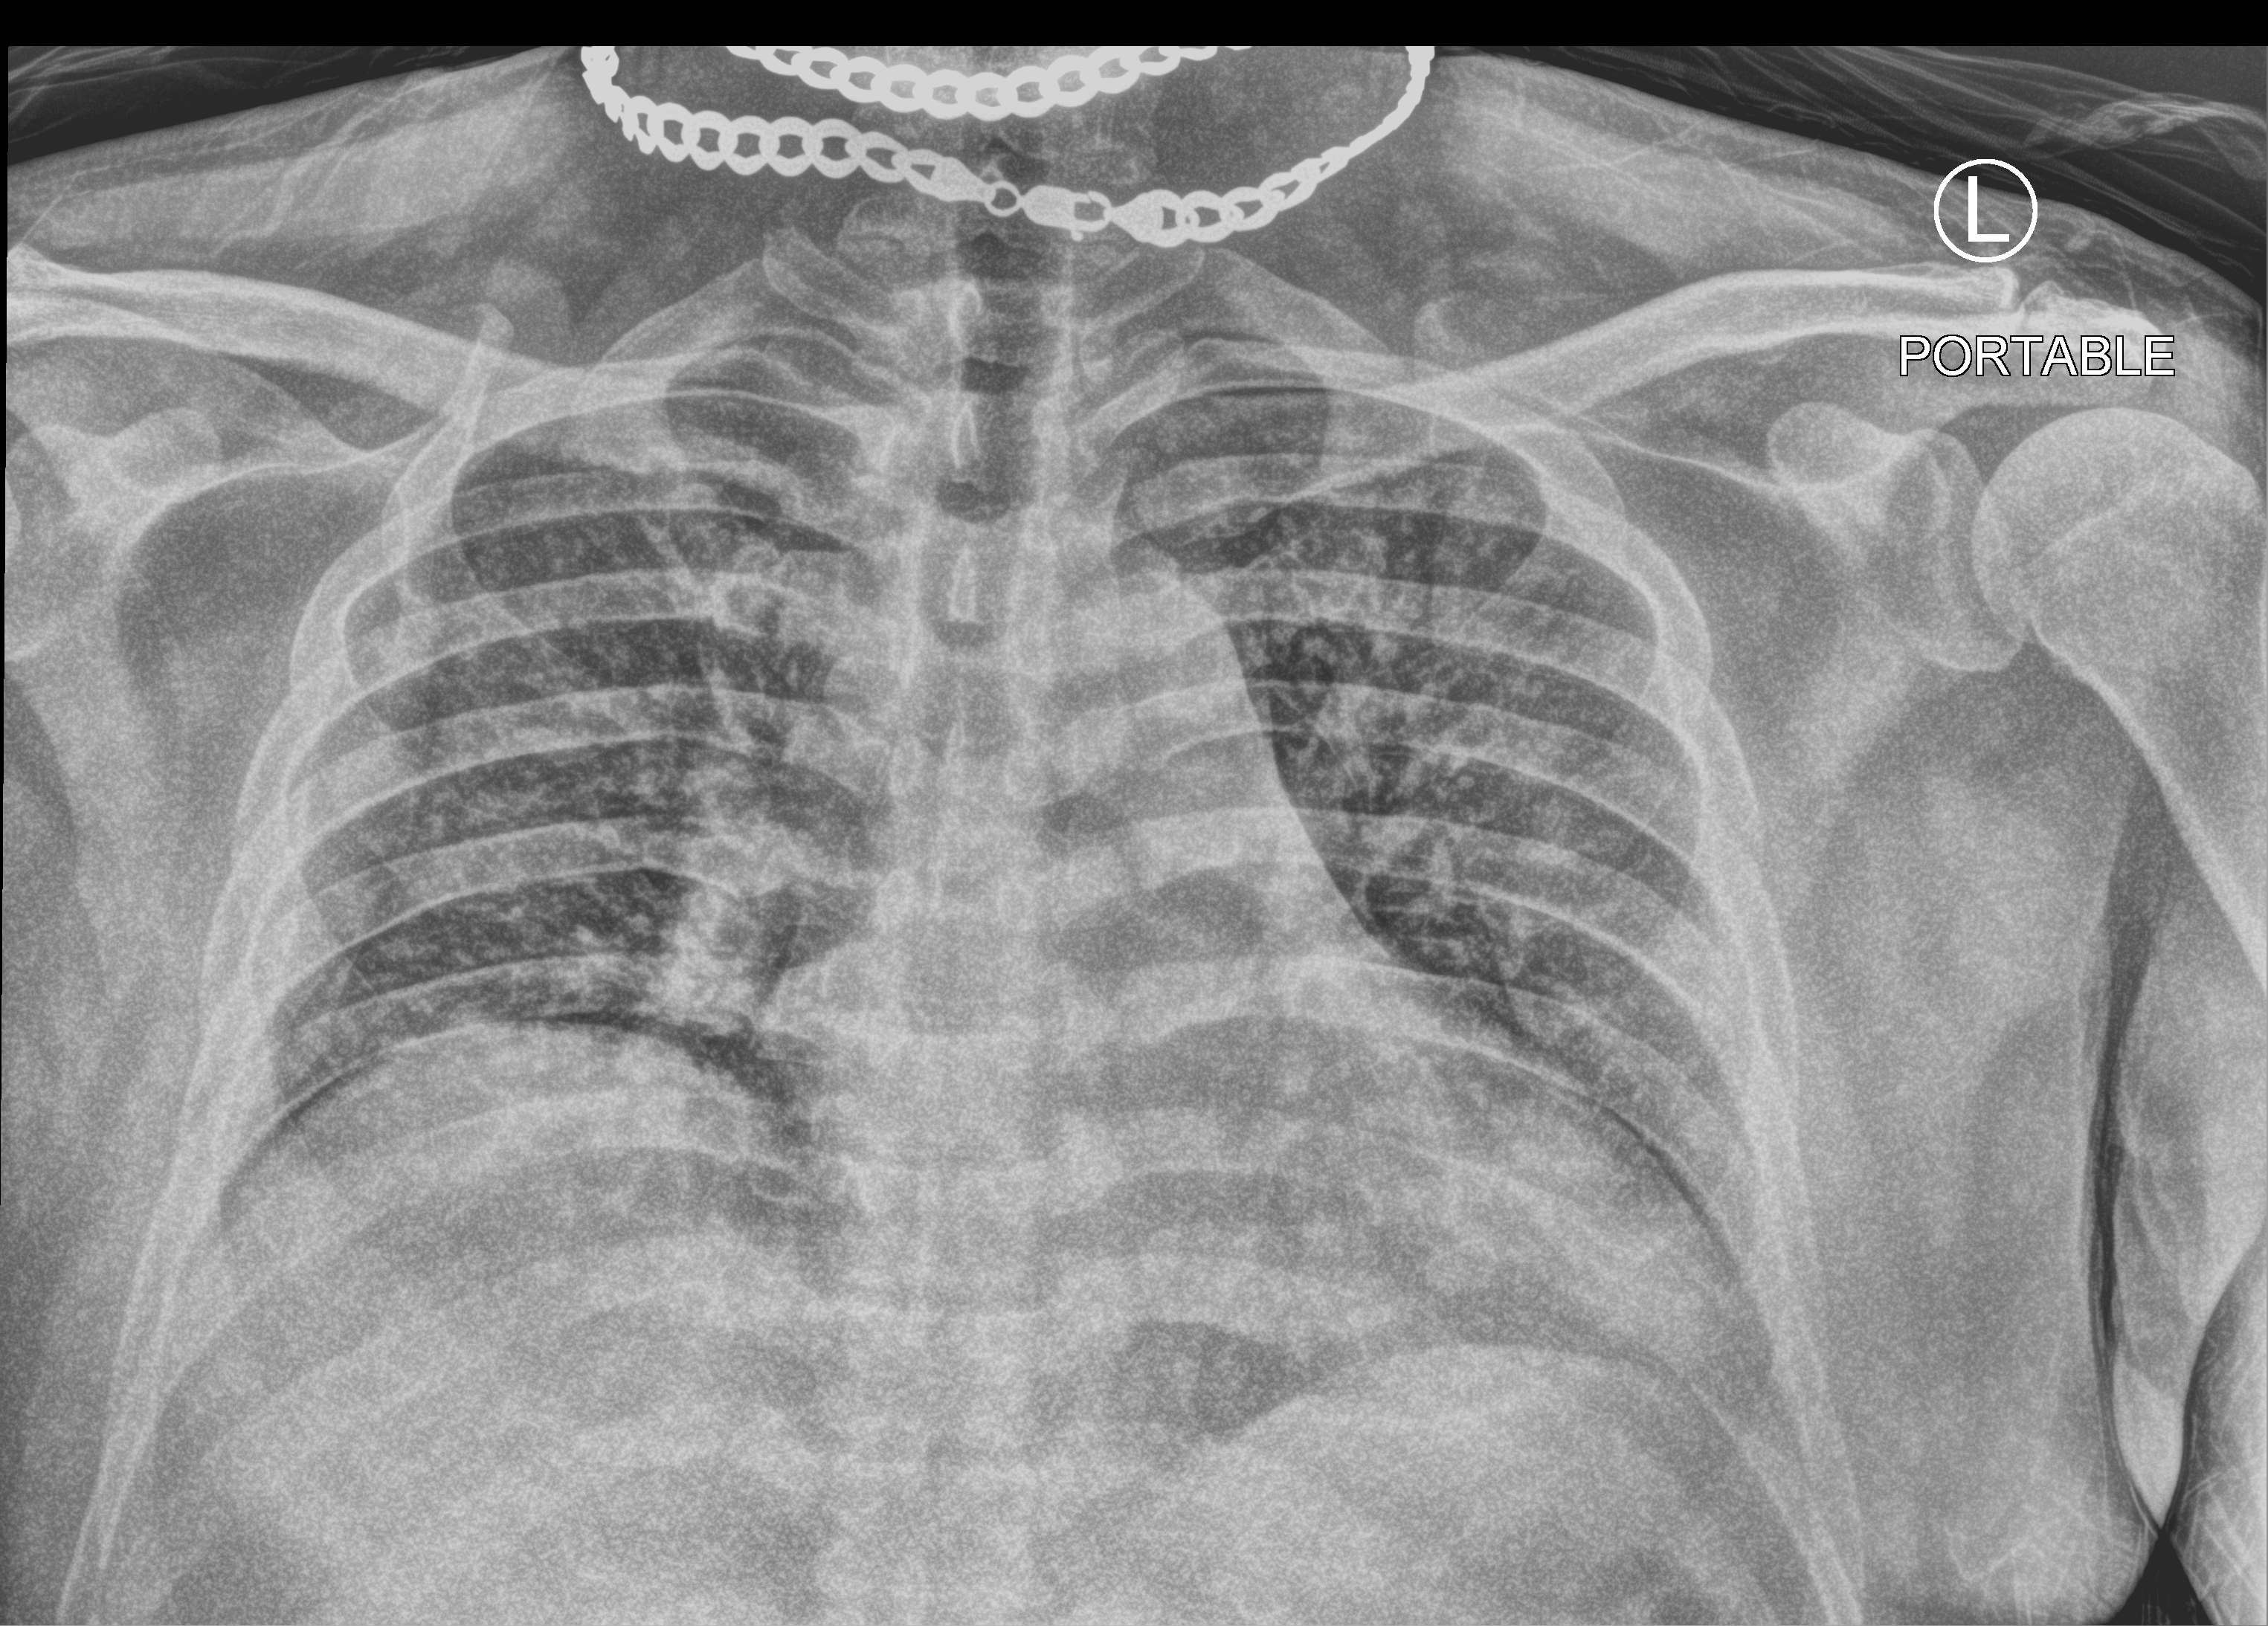
Bedside chest radiograph (computed radiography), anteroposterior (AP) projection. Male patient hospitalised with COVID-19, age 18–59 years.
Admission-level facts for this patient (not findings on this image; timing relative to this image not recorded): mechanically ventilated during this hospital stay: no.